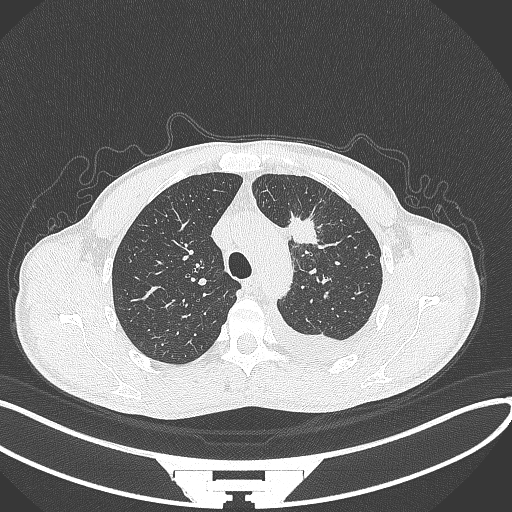
Chest CT, one axial slice. Slice 254 of 371 in the series (ordered by position). Reconstruction kernel B70f. Lung window (W 1500 / L -600 HU). 1 mm slice thickness. 512 × 512 image matrix, field of view 400 × 400 mm. Patient: male, 49 years. From the clinical record (not read from this slice): clinical TNM (as recorded): T1c N1 M1.
Outlined on this slice (bounding box drawn by a radiologist):
- lung tumour (recorded histology: adenocarcinoma): bounding box <284,212,324,256> (left, top, right, bottom; pixels)